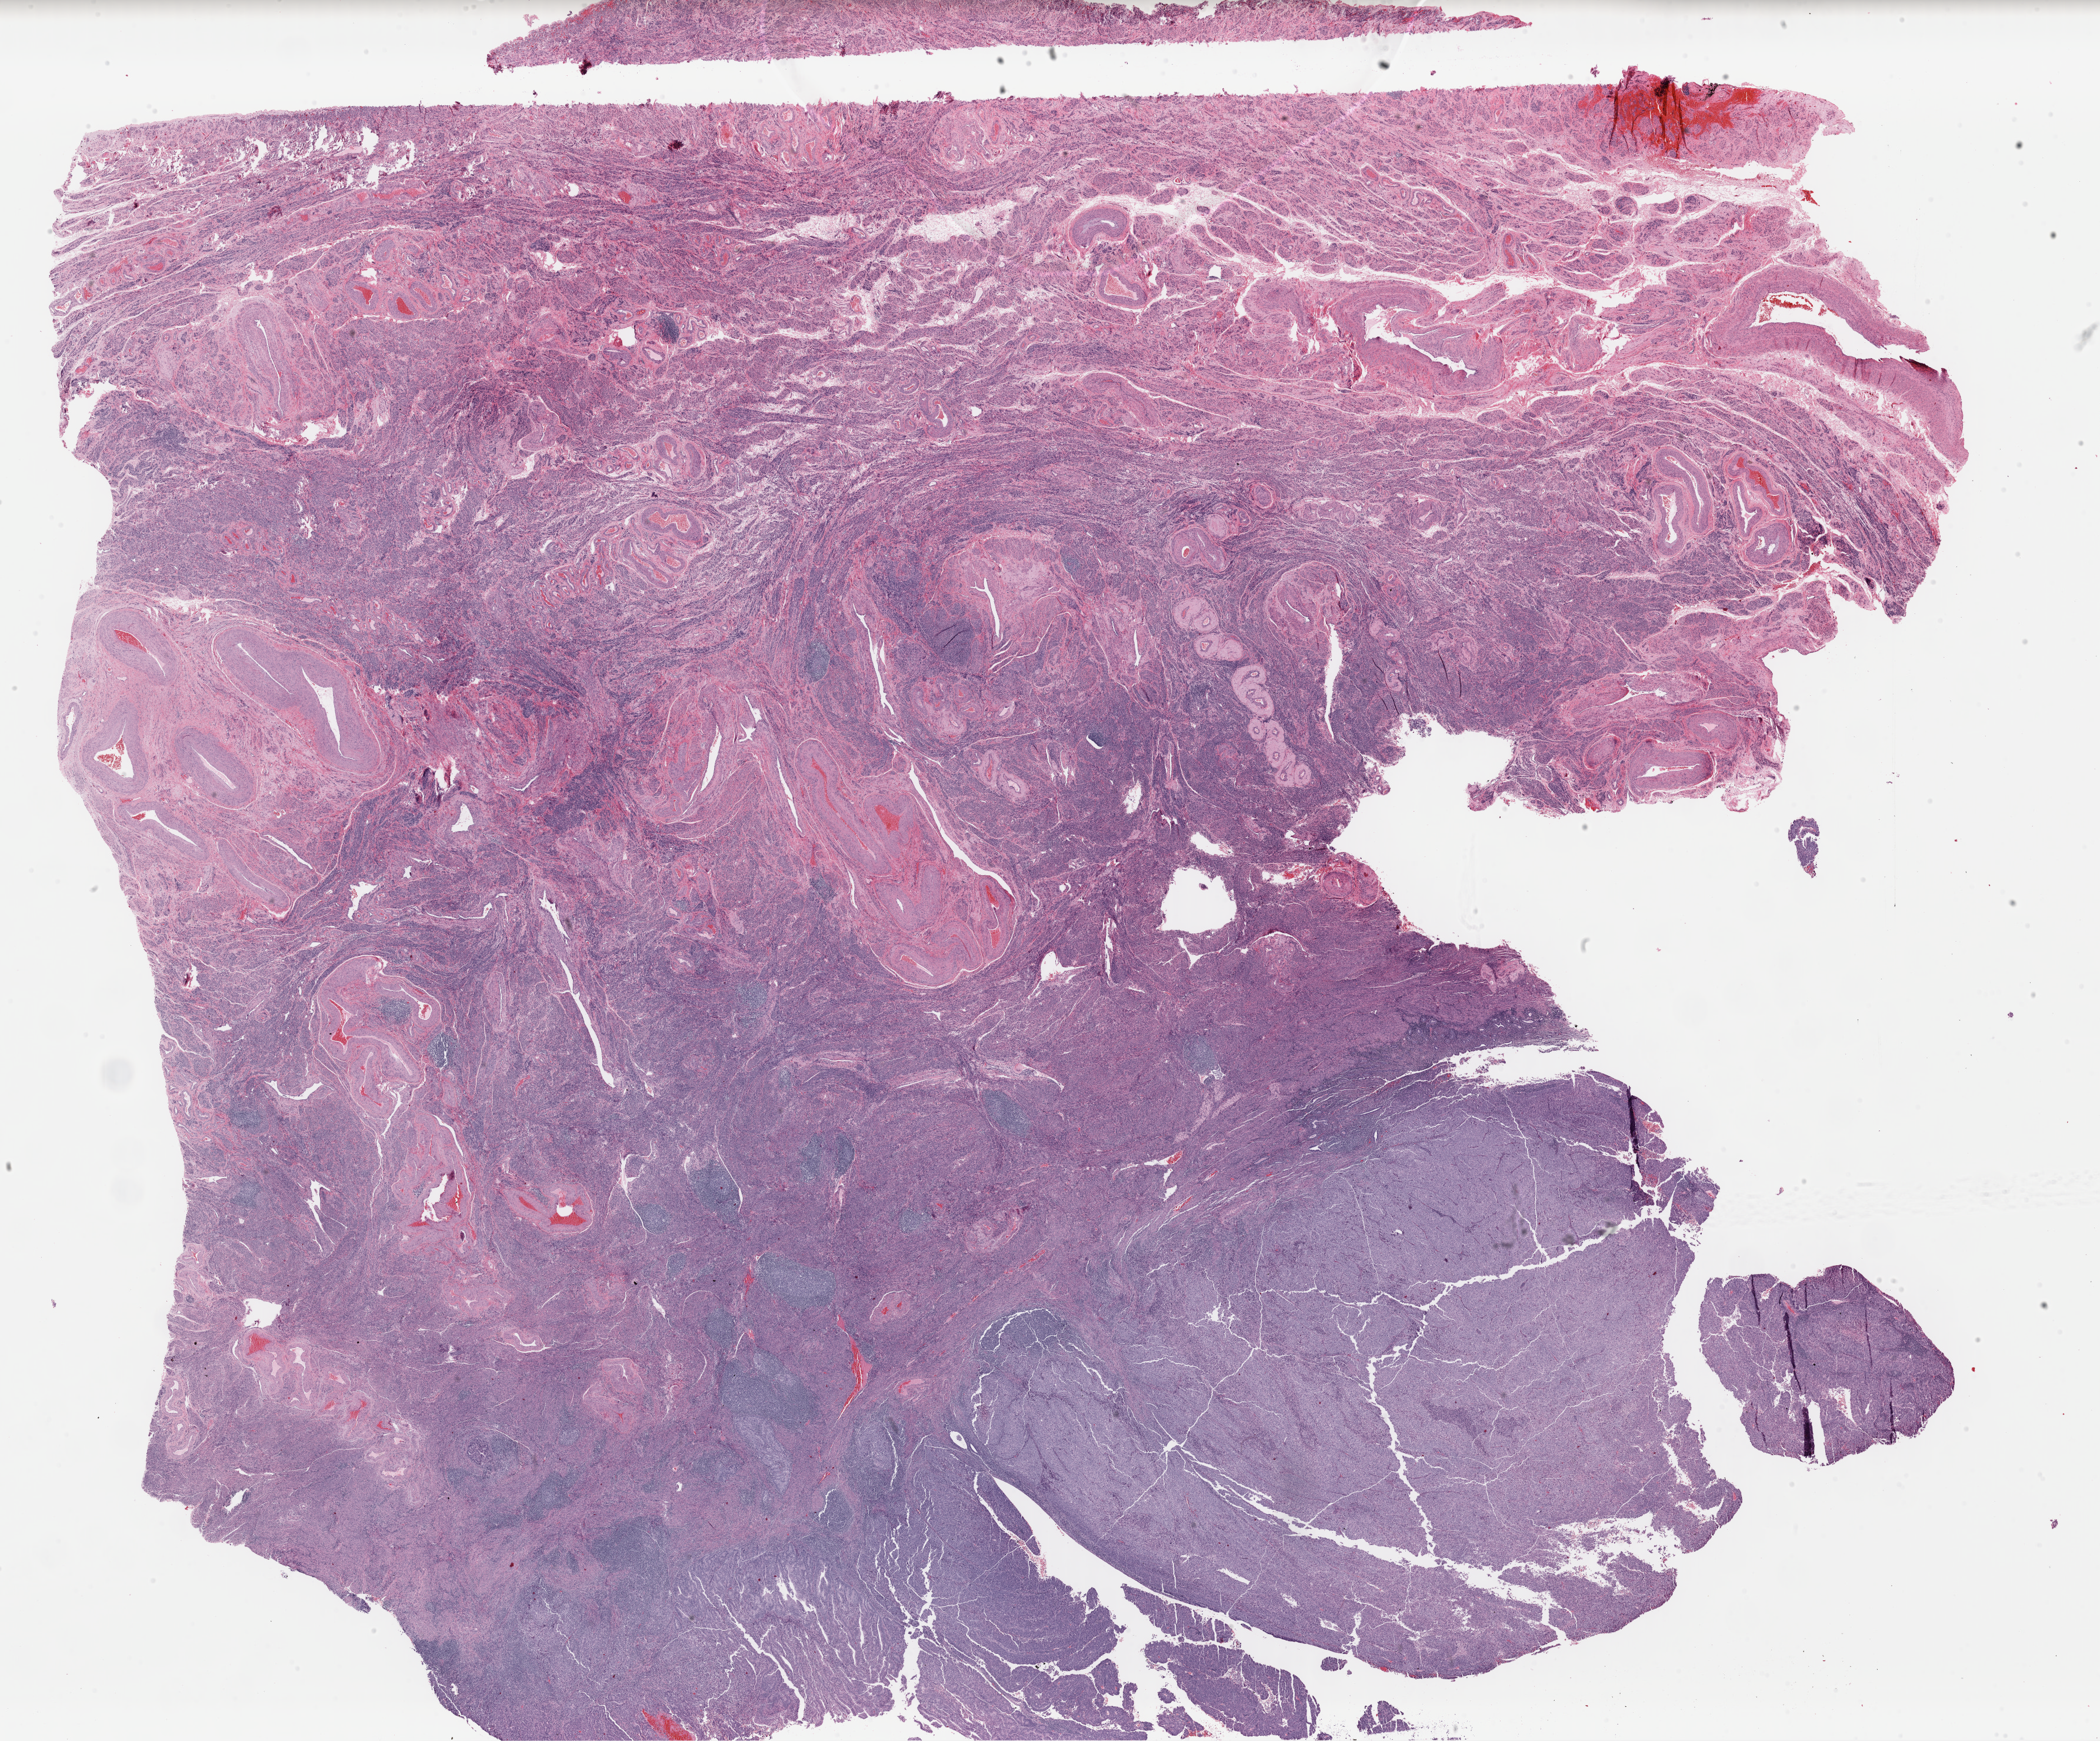
Whole-slide histology image, Hematoxylin and eosin (H&E) stained — whole scanned area (about 28.2 x 23.4 mm, slide scanned at 40x) shown as a low-resolution overview, formalin-fixed paraffin-embedded (FFPE) diagnostic section, uterus, primary tumour sample. Female, age 47 years at initial diagnosis. Histologic grade: high grade.
FIGO stage: IA. Histologic diagnosis: Serous cystadenocarcinoma, NOS.